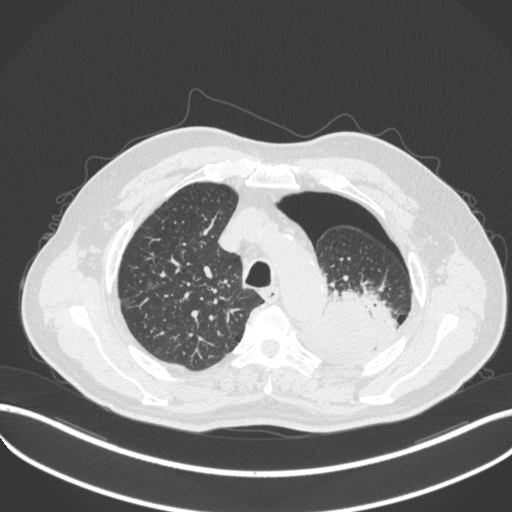
Chest CT, one axial slice. 120 kVp. Lung window (W 1500 / L -600 HU). 512 × 512 image matrix, field of view 400 × 400 mm. Male patient, age 76 years. Case-level facts recorded for this patient, not image findings: clinical TNM (as recorded): T3 N0 M1b.
Annotated regions visible in this slice (bounding box drawn by a radiologist):
- lung tumour (recorded histology: adenocarcinoma): box from (x=316, y=286) to (x=379, y=366) px